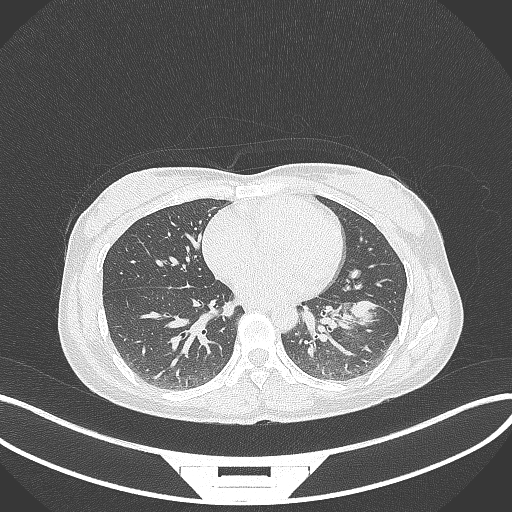
Chest CT, one axial slice; reconstruction kernel B70f; 120 kVp; lung window (W 1500 / L -600 HU); 1 mm slice thickness; 512 × 512 image matrix. Patient: female, 41 years. Case-level facts recorded for this patient, not image findings: clinical TNM (as recorded): T2a N3 M1b.
Annotated regions visible in this slice (rectangle marked by the reading radiologist):
- lung tumour (recorded histology: adenocarcinoma): box from (x=346, y=299) to (x=380, y=322) px